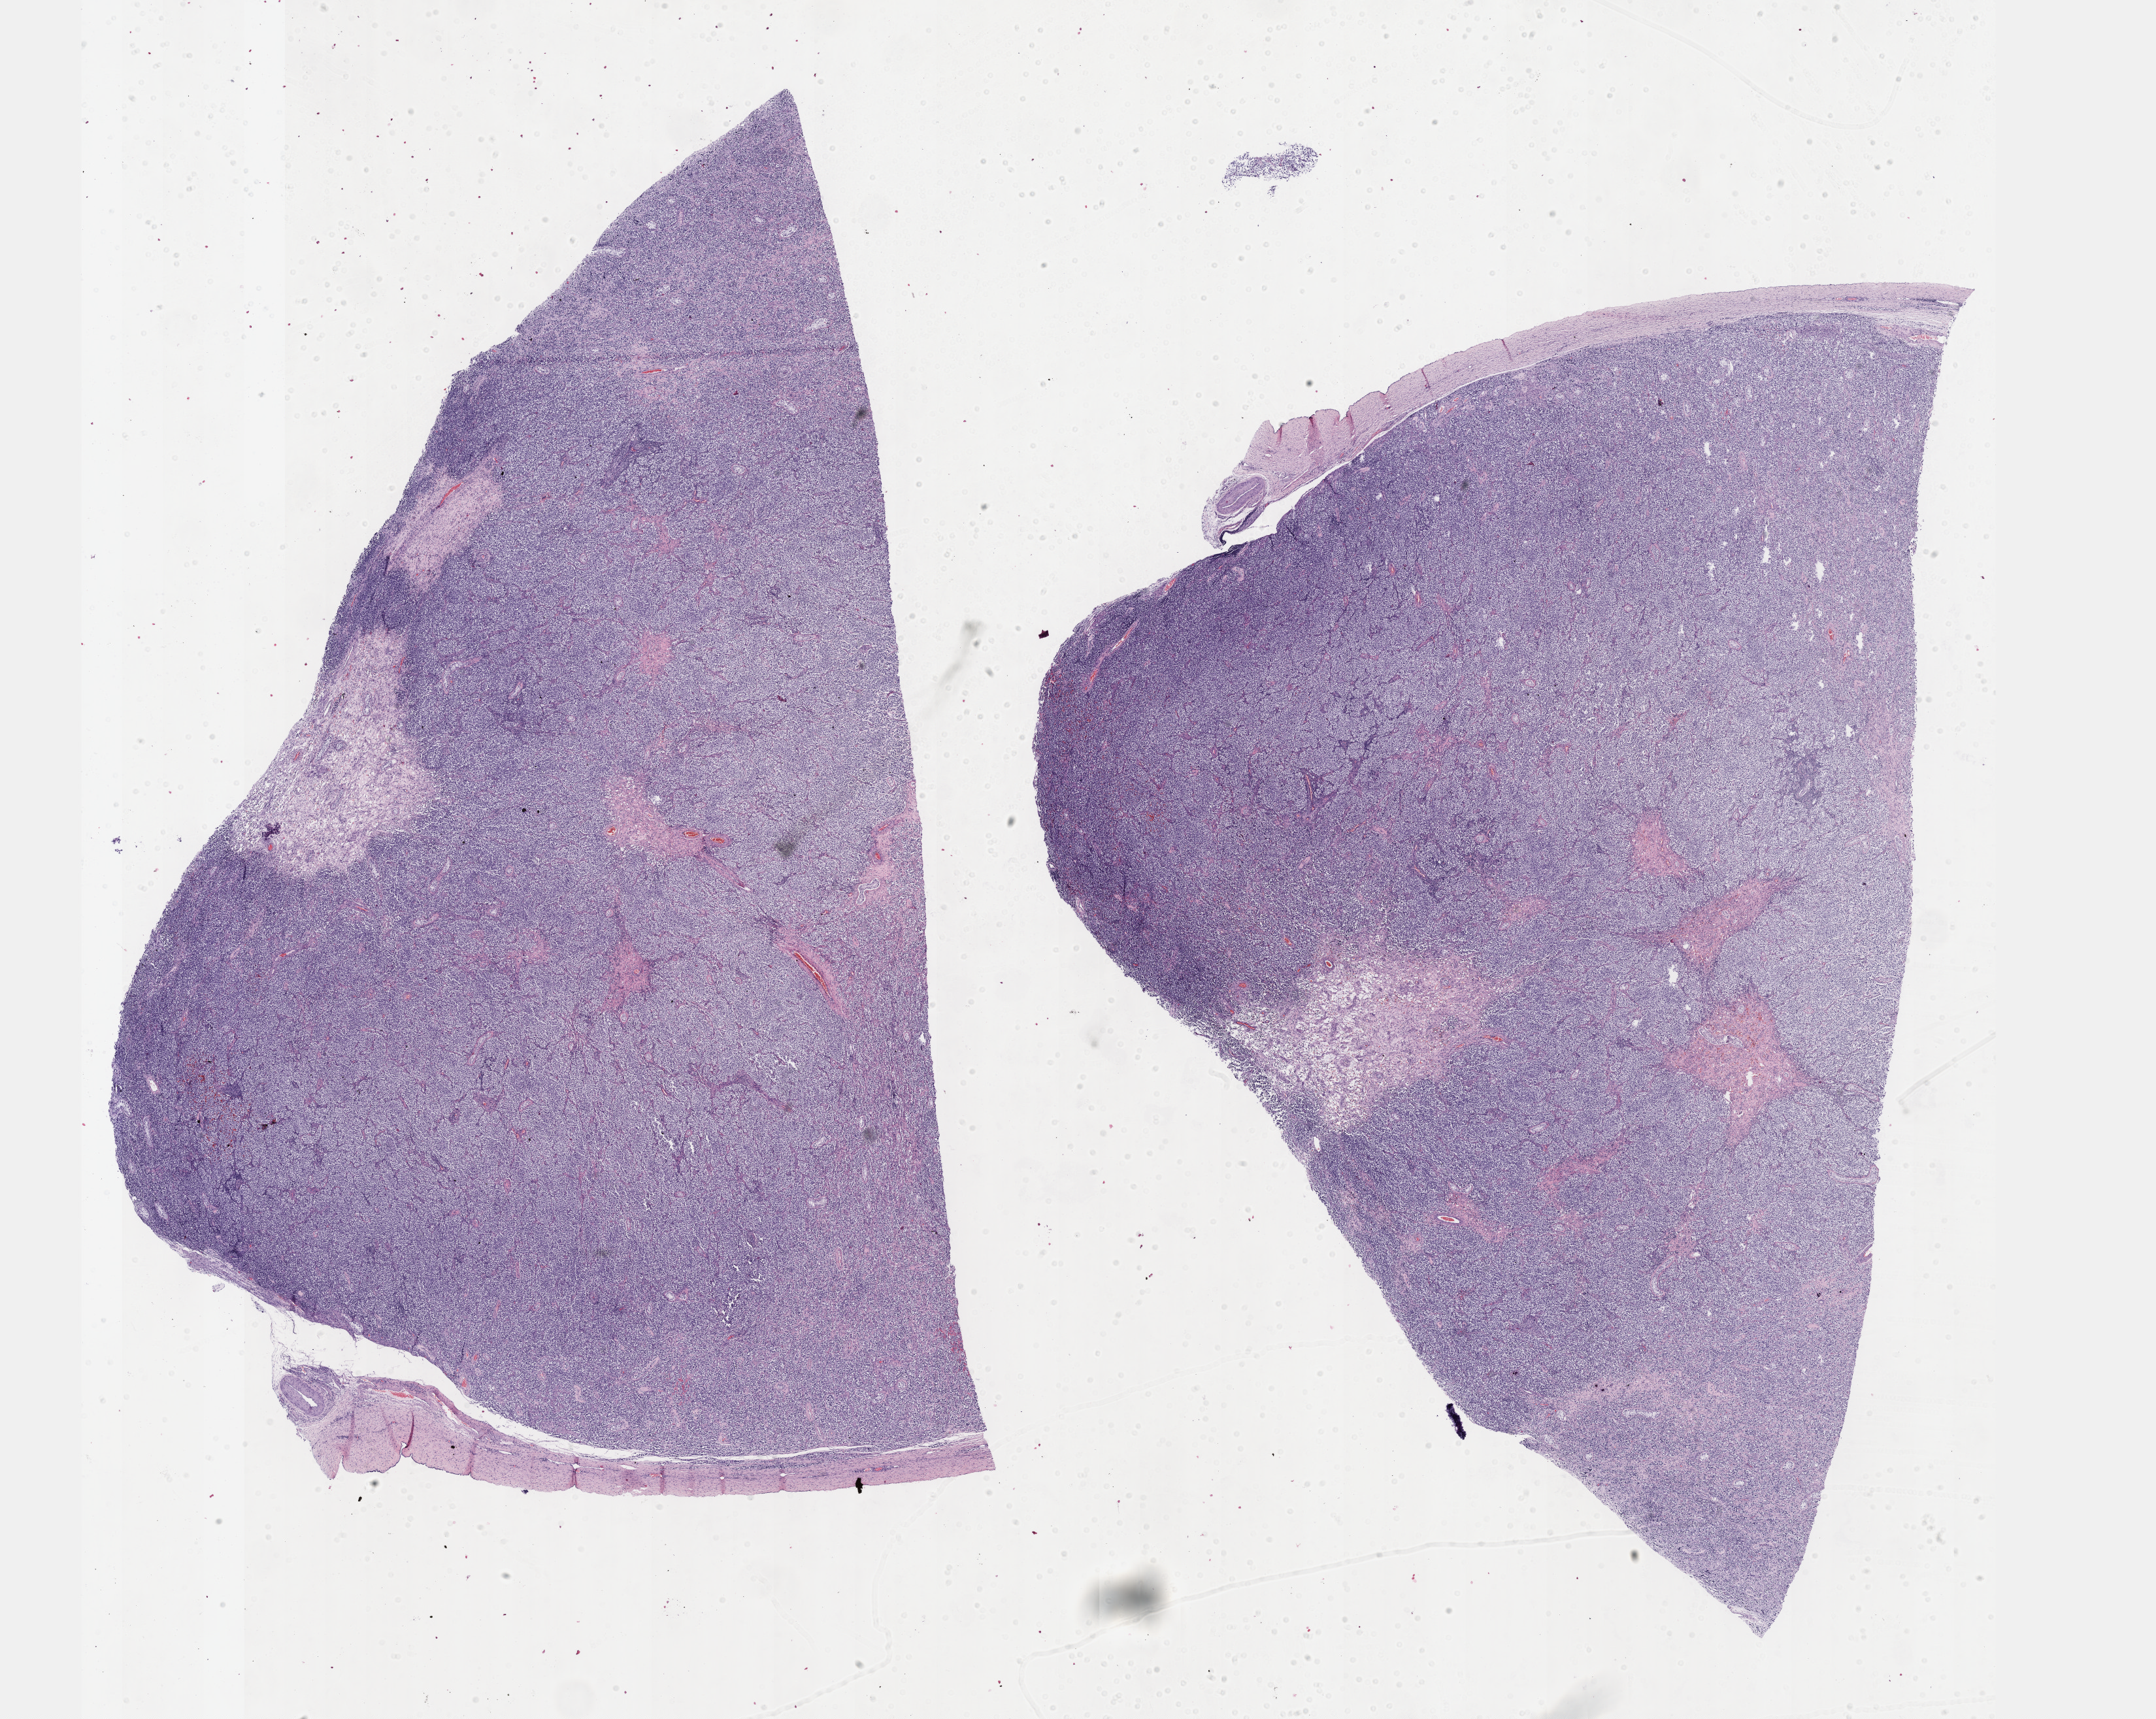
Digitized H&E tissue section (whole slide) — whole scanned area (about 26.7 x 21.3 mm, acquisition: 40x scan) shown as a low-resolution overview; FFPE section; primary tumour sample from the testis. Male patient; age at initial diagnosis 30 years.
Histologic diagnosis: Mixed germ cell tumor.